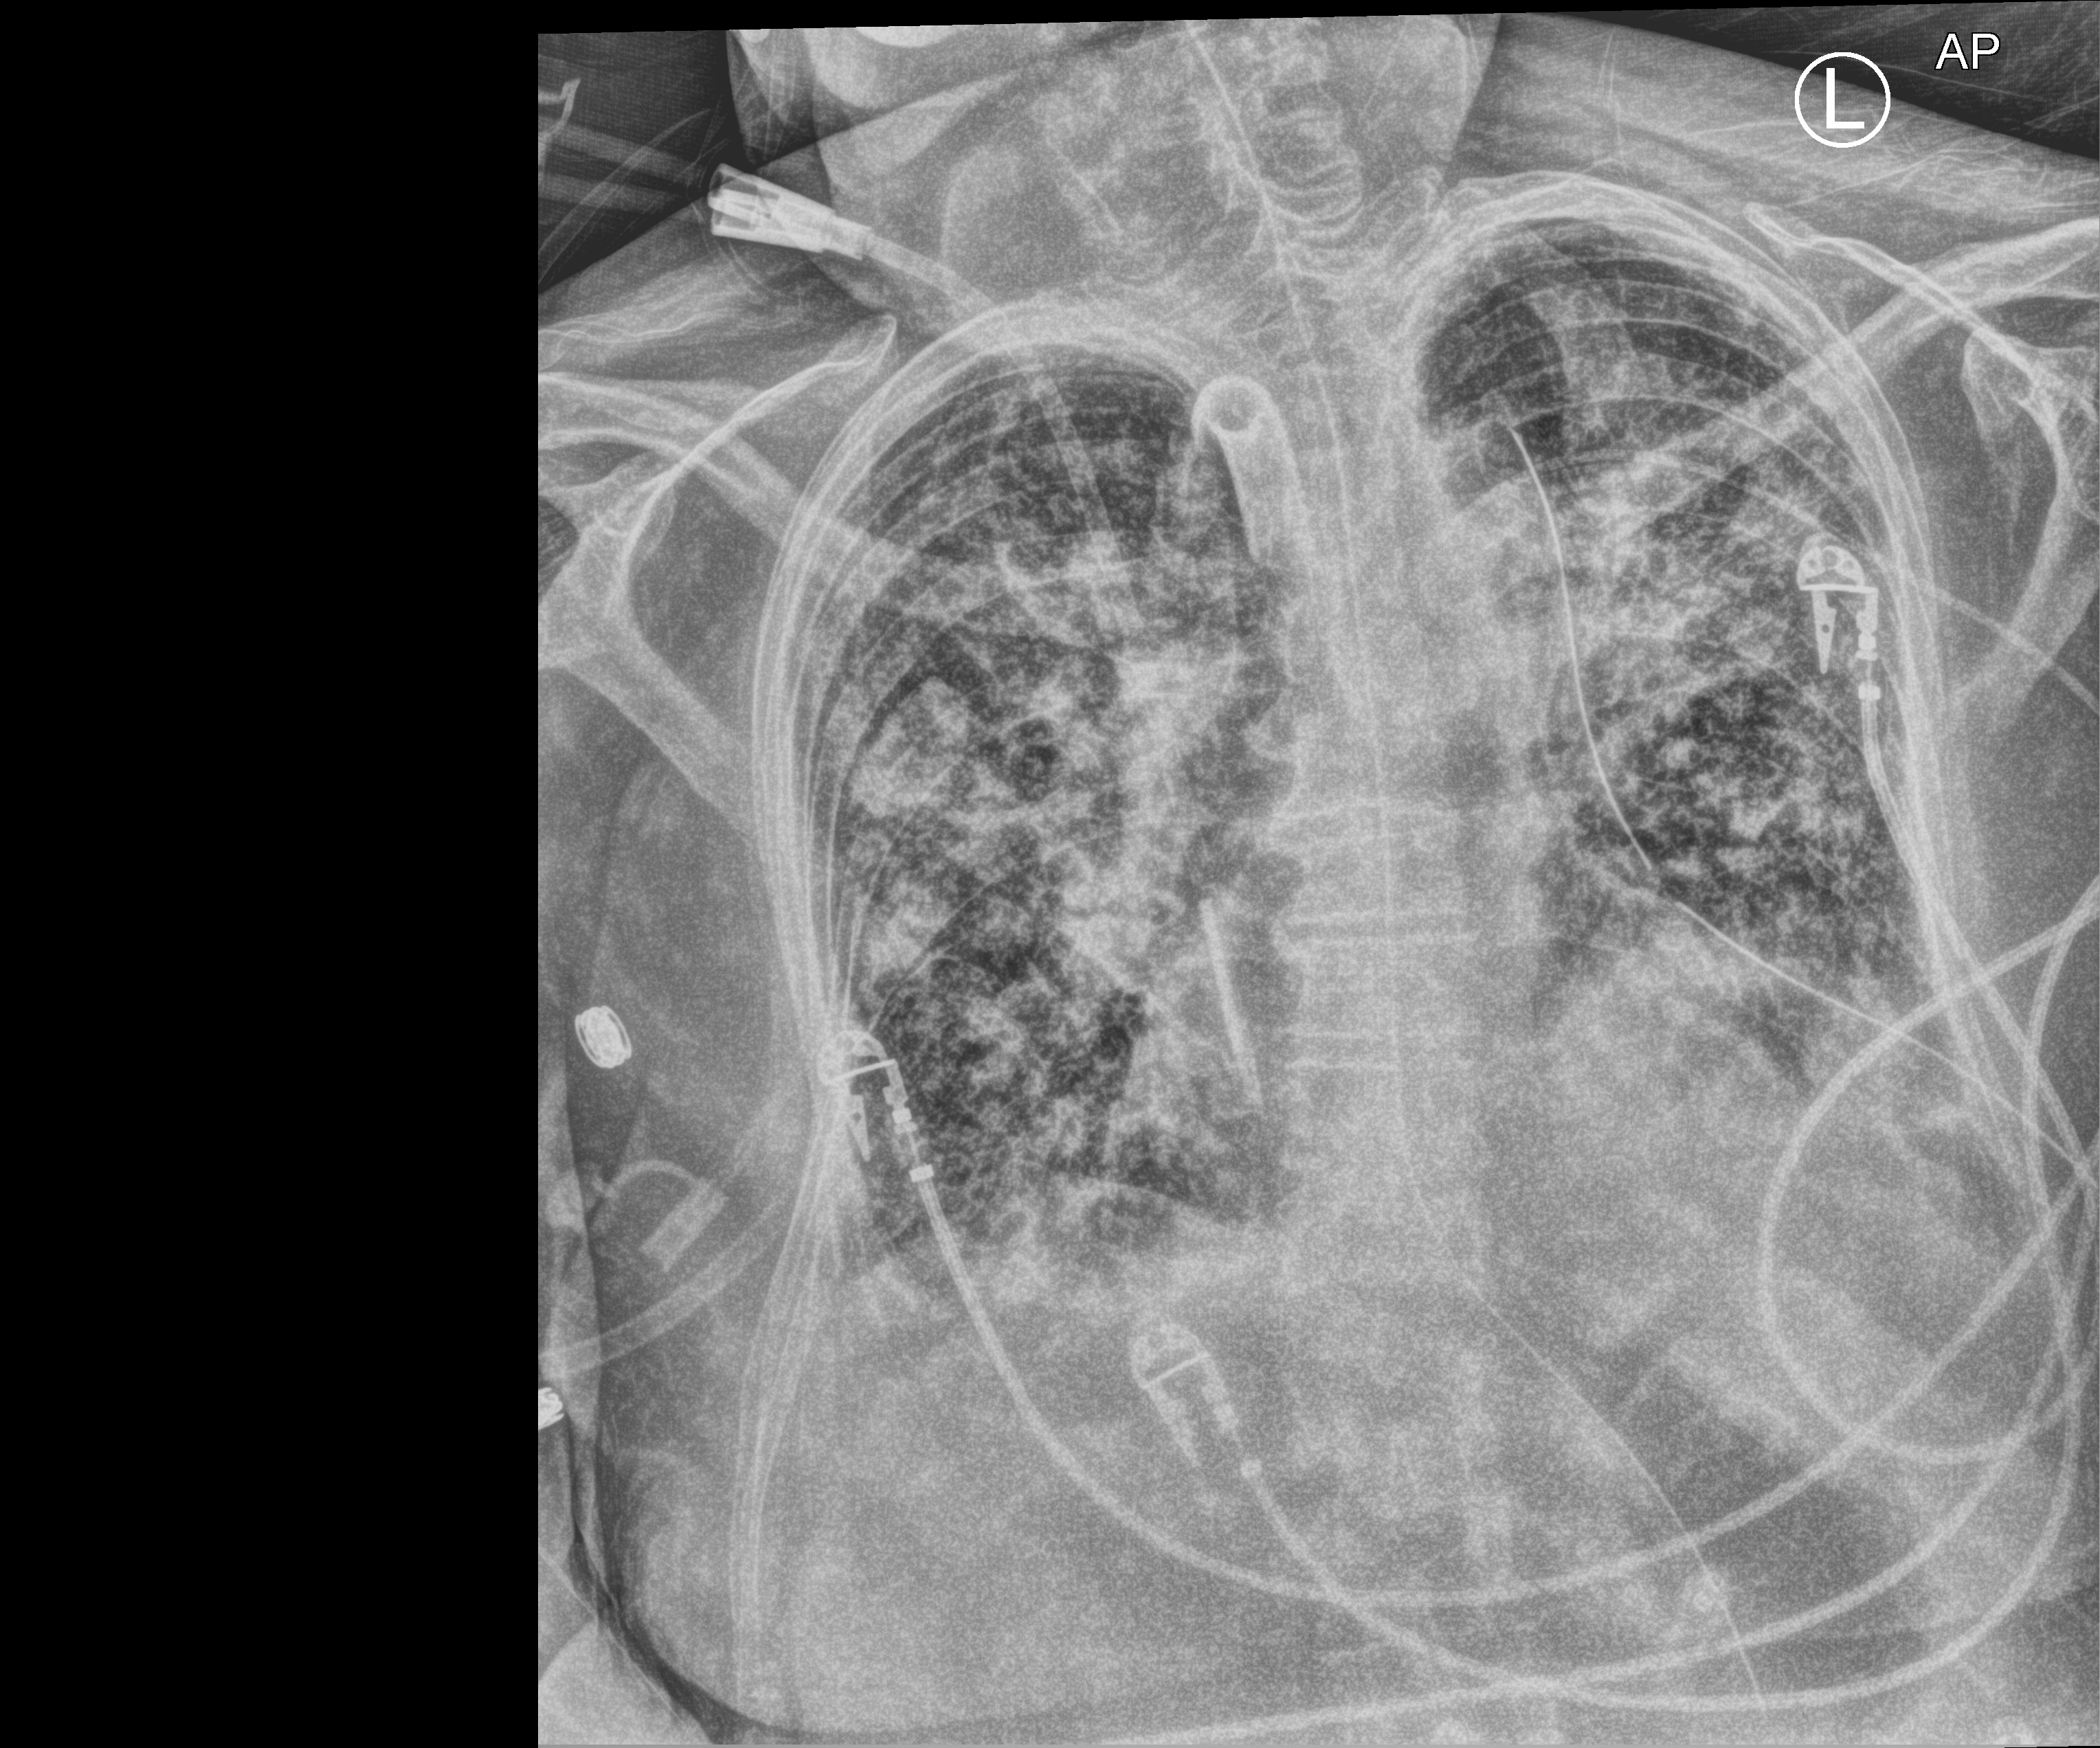
Chest X-ray (portable), anteroposterior (AP) projection. Female patient hospitalised with COVID-19, age 75–90 years.
Hospital-stay facts (about this admission, not read from this image; timing relative to this image not recorded):
- smoking status (admission record): former